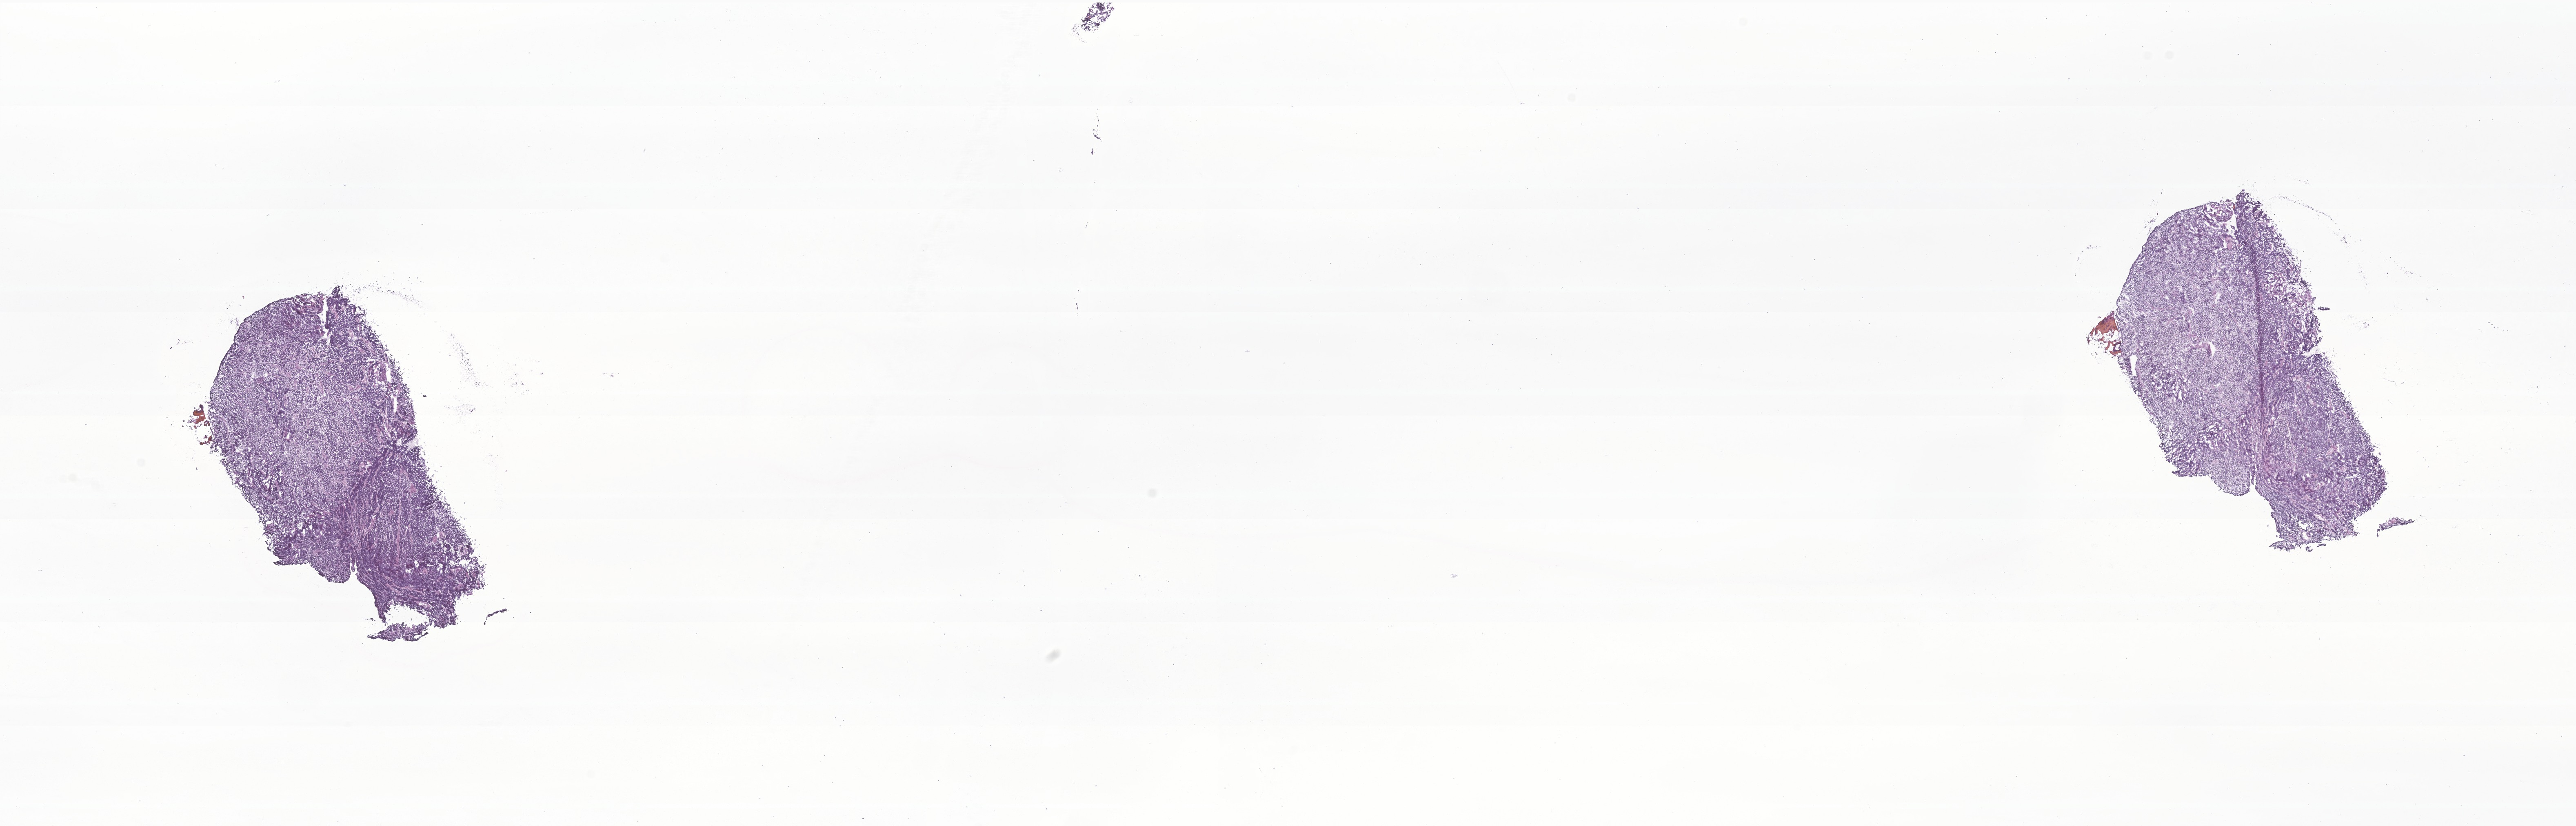
Whole-slide image, haematoxylin and eosin stain of tumor tissue from the brain — whole scanned area (about 26.6 x 8.5 mm) shown as a low-resolution overview. Frozen section. Patient: male, age 188 months (15 years 8 months).
Diagnosis: Medulloblastoma, NOS.